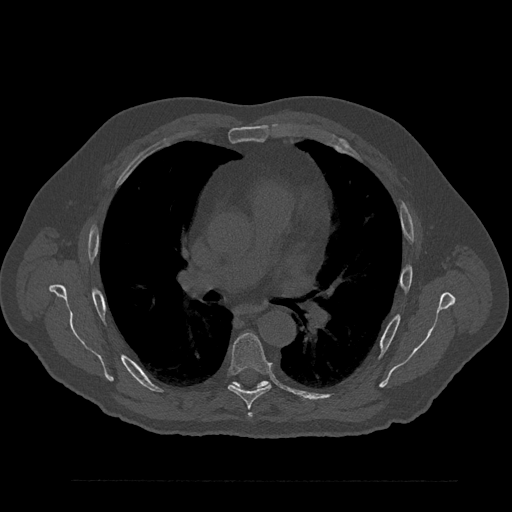
CT including the spine, one axial slice; position 546 of 797 along the scan axis; reconstruction kernel Br40s/3; bone window (W 1800 / L 400 HU); 0.5 mm slice thickness; 512 × 512 image matrix. Male patient, age 61 years. Case-level facts recorded for this patient, not image findings: primary cancer: prostate.
Outlined on this slice (semi-automatic segmentation, software-assisted and operator-edited):
- T6 vertebra: box from (x=228, y=333) to (x=272, y=417) px
- T7 vertebra: (x=237, y=381)–(x=268, y=388)